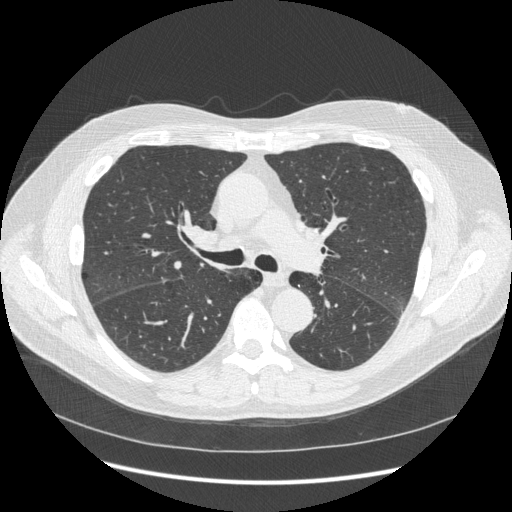
Low-dose screening chest CT, axial slice; second screening round (one year after baseline); lung window (W 1500 / L -600 HU); standard (soft-tissue) reconstruction kernel (STANDARD). Male participant, aged 59 years at enrolment. Current smoker at enrolment.
- Expert reader's lesion annotation, box from (x=168, y=212) to (x=235, y=261) px.
- The exam's reader record, not a measurement of the box and not confirmed to be the same lesion: non-calcified nodule or mass ≥4 mm, lingula, 5 × 5 mm, smooth margins, soft tissue attenuation, pre-existing on the prior screen: yes; interval growth: no.
- Note: the box lies in the patient's right hemithorax on this image, whereas the reader's record names the left lung; they may be different findings.